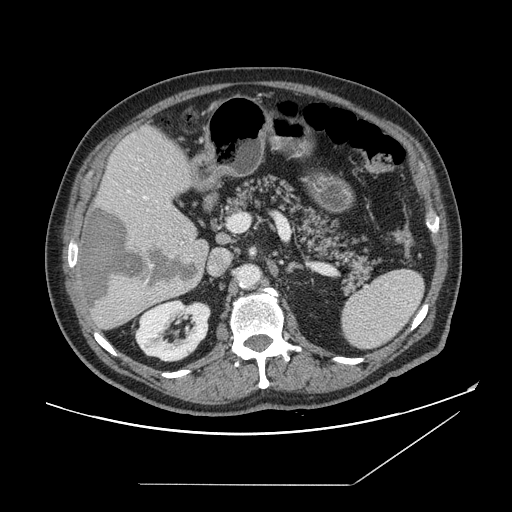
Contrast-enhanced abdominal CT, one axial slice; position 84 of 166 along the scan axis; intravenous contrast given; soft-tissue window (W 400 / L 40 HU); 512 × 512 image matrix, field of view 416 × 416 mm. Male patient, age 80 years. From the clinical record (not read from this slice): diagnosis: colorectal cancer liver metastases, imaged before liver resection; multiple liver metastases: no; largest metastasis: 2.2 cm.
Outlined on this slice (manually delineated by an expert):
- hepatic veins: bounding box <136,169,147,200> (left, top, right, bottom; pixels)
- liver: <78,128,209,330>
- planned liver remnant (the part of the liver to remain after resection): <101,127,199,237>
- portal vein (with intrahepatic branches): <128,191,231,229>
- liver metastasis: <82,207,199,308>